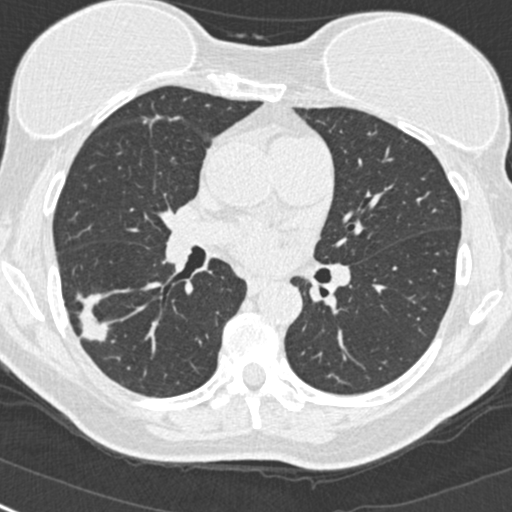
Low-dose screening chest CT, one axial slice; slice 142 of 268 in the series (ordered by position); lung window (W 1500 / L -600 HU); 512 × 512 image matrix, field of view 296 × 296 mm.
Structures marked on this image (outlined manually by an expert reader):
- lesion 1 (tumor, upper lobe of right lung): box from (x=77, y=294) to (x=109, y=341) px